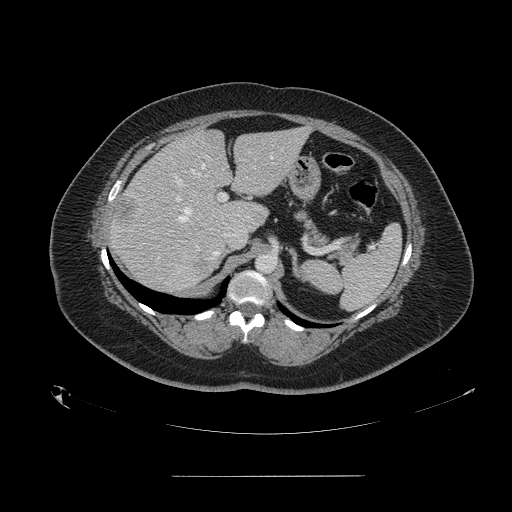
Contrast-enhanced abdominal CT, one axial slice. Slice 100 of 164 in the series (ordered by position). 120 kVp. Intravenous contrast given. Soft-tissue window (W 400 / L 40 HU). 2.5 mm slice thickness. 512 × 512 image matrix. Female patient, age 52 years. From the clinical record (not read from this slice): diagnosis: colorectal cancer liver metastases, imaged before liver resection; multiple liver metastases: yes; largest metastasis: 3.5 cm.
Outlined on this slice (expert manual segmentation):
- hepatic veins: bounding box [x1, y1, x2, y2] px = [178, 156, 273, 222]
- liver: [110, 129, 308, 292]
- planned liver remnant (the part of the liver to remain after resection): [174, 129, 307, 229]
- portal vein (with intrahepatic branches): [173, 175, 227, 202]
- liver metastasis: [192, 260, 208, 271]
- liver metastasis: [251, 212, 262, 224]
- liver metastasis: [114, 197, 136, 225]